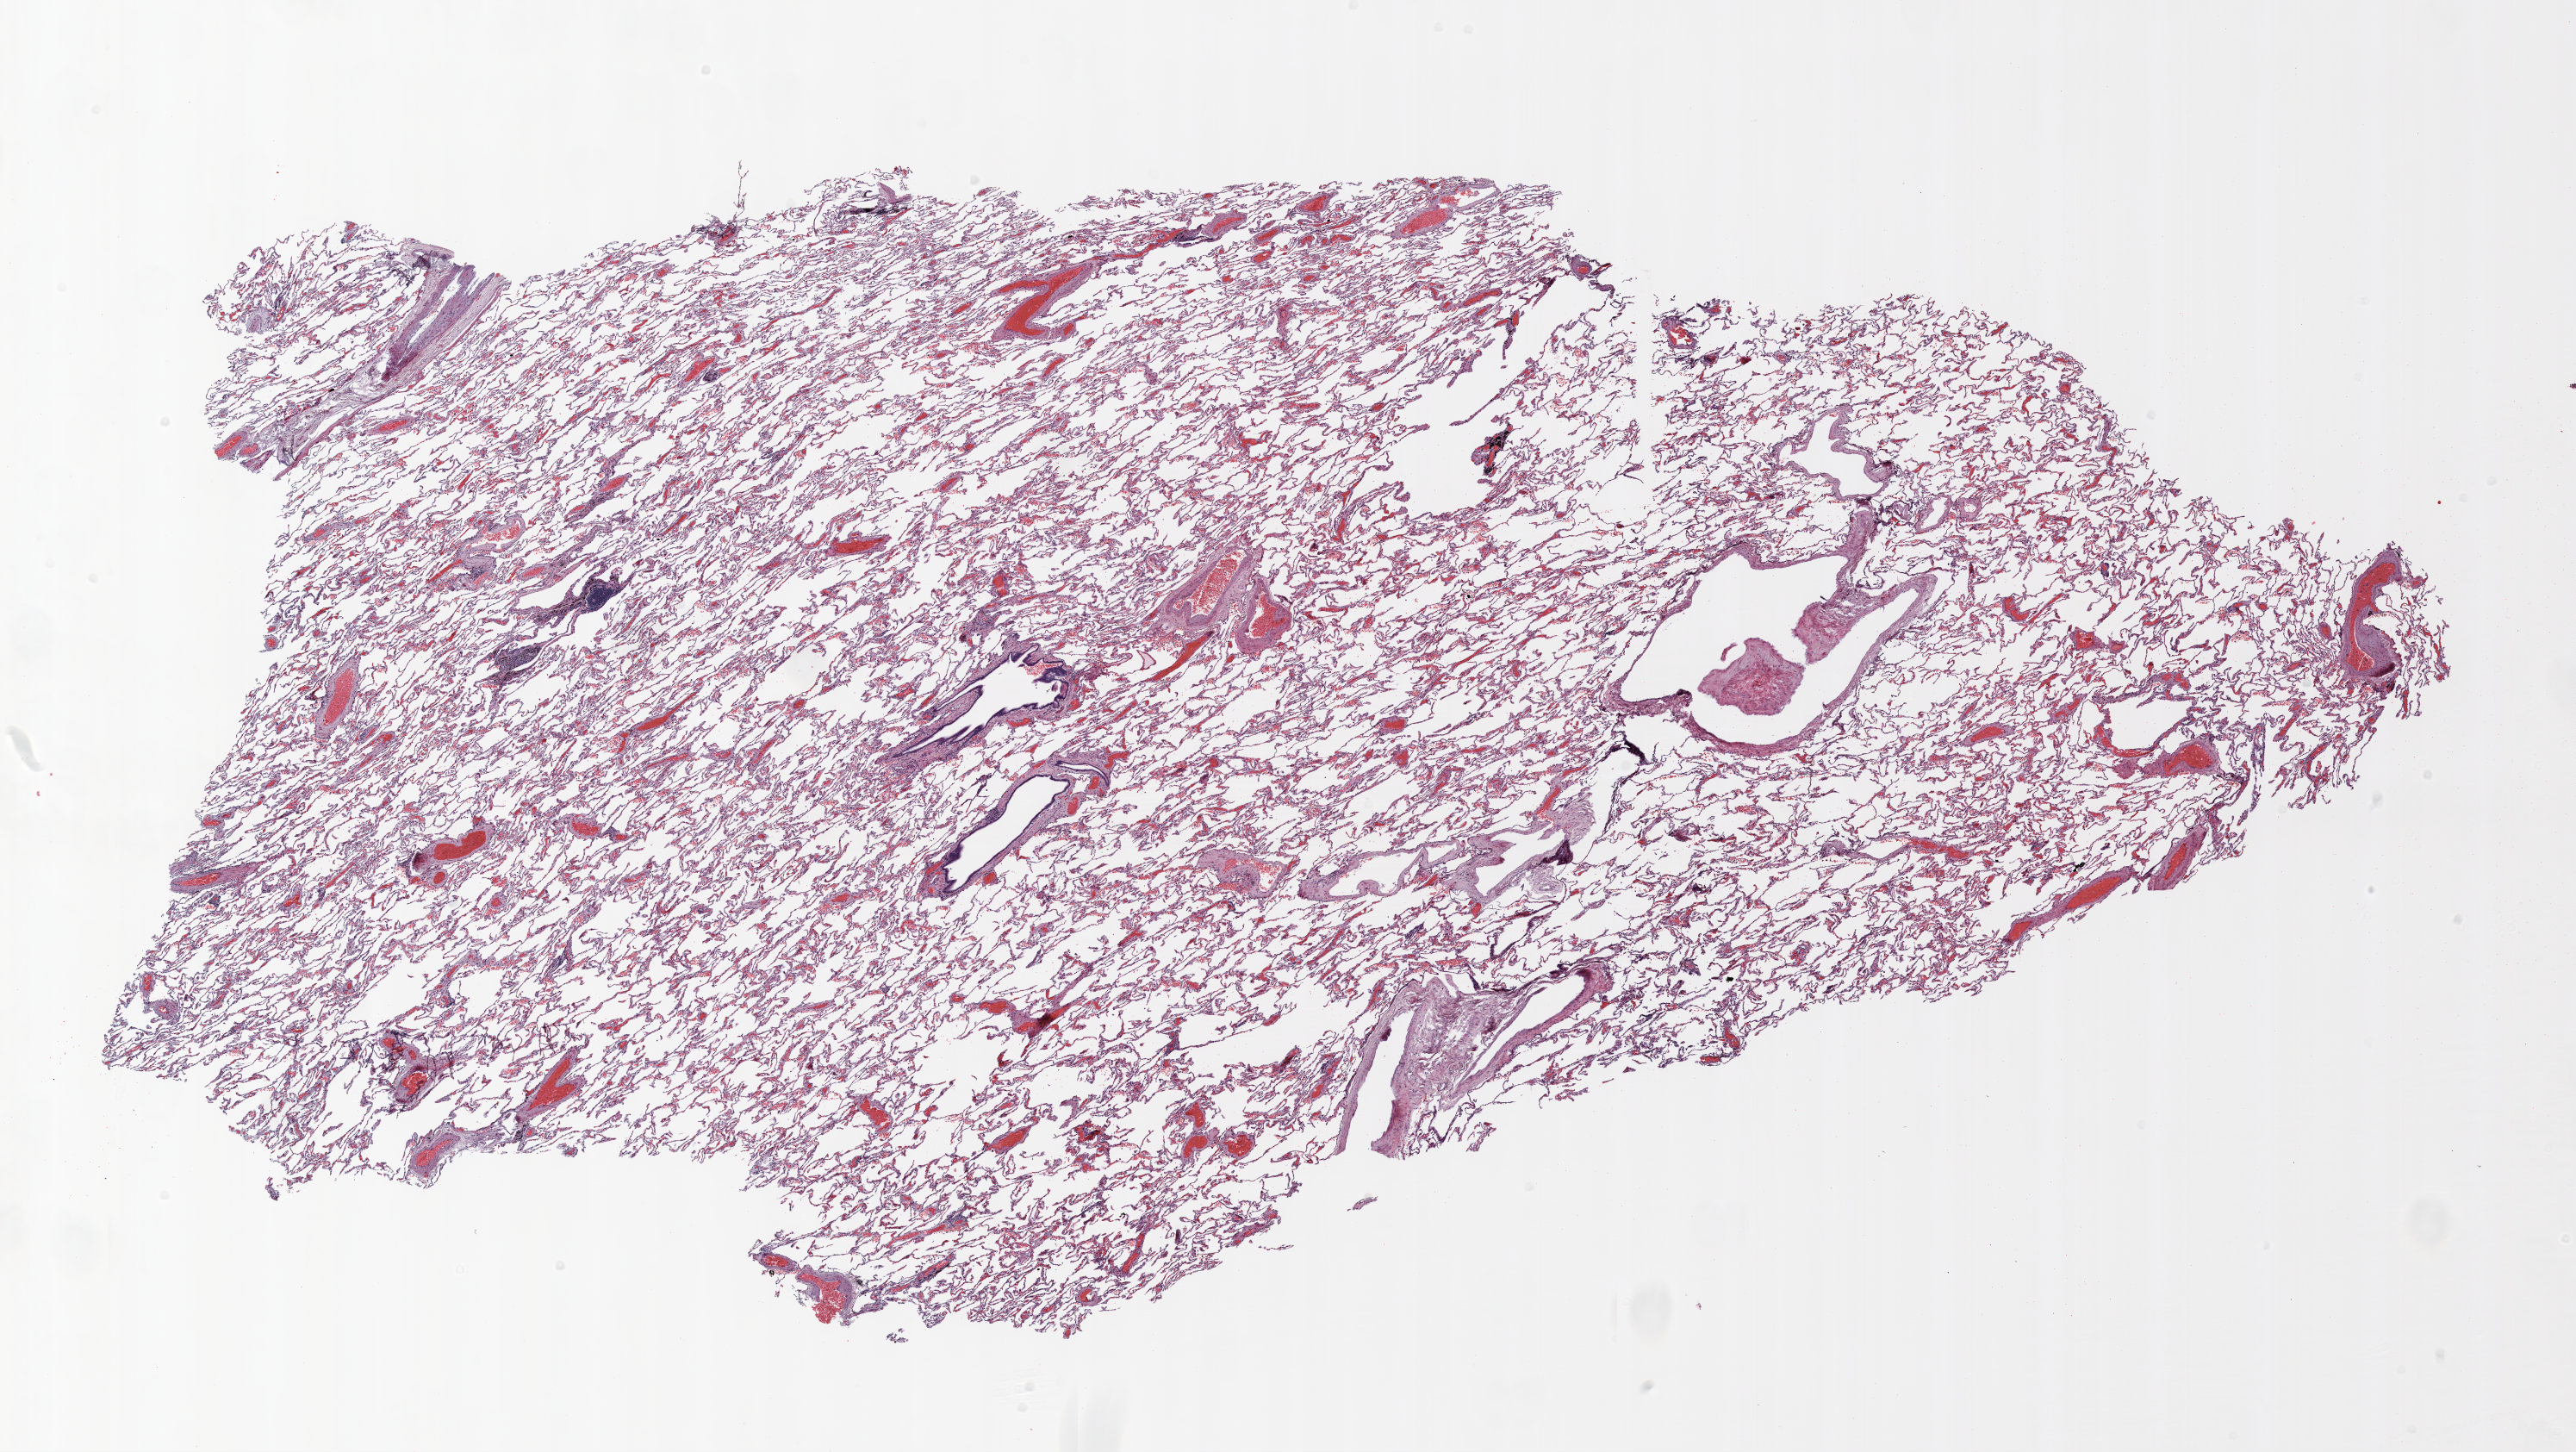
Whole-slide histology image, H&E-stained, whole scanned area (about 24.0 x 13.5 mm) shown as a low-resolution overview; FFPE section; lung. Male patient, aged 69 at enrolment. Former smoker at enrolment. Grade: well differentiated (G1).
- participant's lung-cancer diagnosis: Bronchiolo-alveolar adenocarcinoma, NOS (ICD-O-3 8250/3)
- primary tumour location (clinical record): right lower lobe
- tumour size (pathology): 23 mm
- ICD-O-3 topography: lower lobe of lung (C34.3)
- stage (AJCC 6th edition): IB